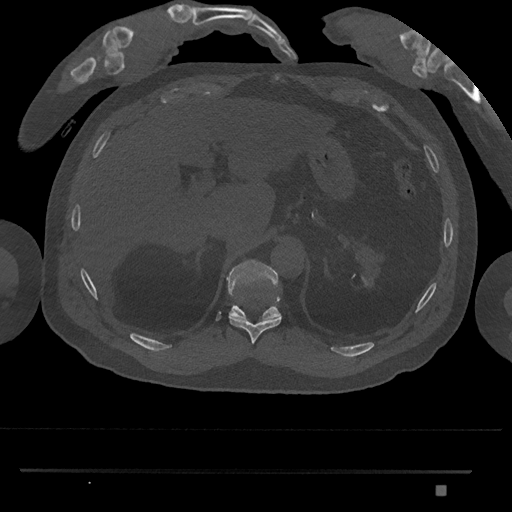
CT including the spine, one axial slice. Slice 980 of 1134 in the series (ordered by position). 120 kVp. Bone window (W 1800 / L 400 HU). 0.5 mm slice thickness. 512 × 512 image matrix, field of view 429 × 429 mm. Male patient, age 65 years. From the clinical record (not read from this slice): primary cancer: prostate.
Outlined on this slice (semi-automatic segmentation, software-assisted and operator-edited):
- T10 vertebra: bounding box [x1, y1, x2, y2] px = [229, 316, 282, 345]
- T11 vertebra: [226, 259, 281, 320]